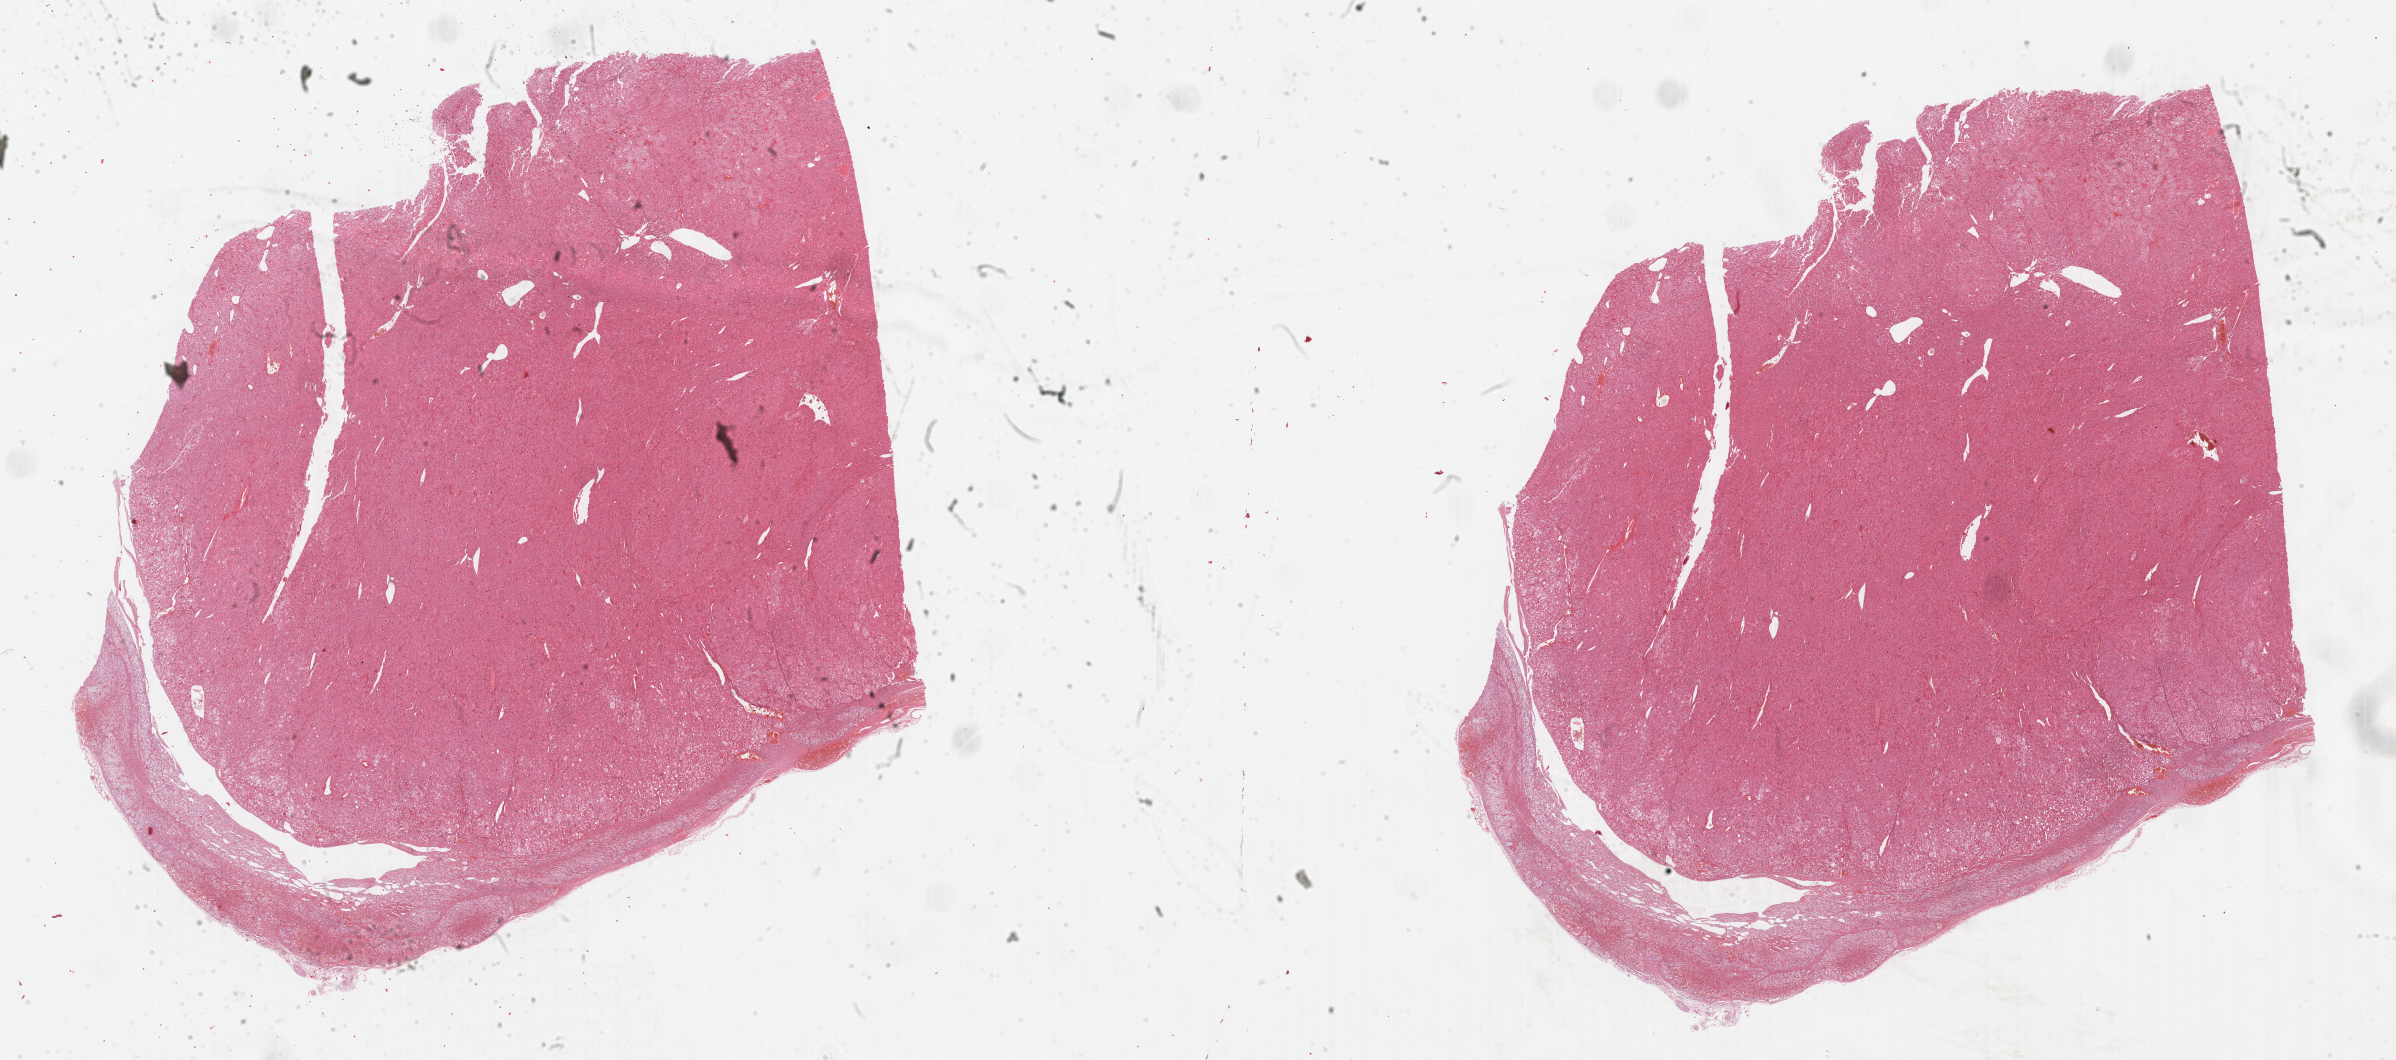
Digitized H&E-stained tissue section (whole slide) — whole scanned area (about 38.8 x 17.1 mm, from a 40x scan) shown as a low-resolution overview. Formalin-fixed paraffin-embedded (FFPE) diagnostic section. Primary tumour sample from the adrenal cortex. Female, age 36 years at initial diagnosis.
Pathologic diagnosis: Adrenal cortical carcinoma.